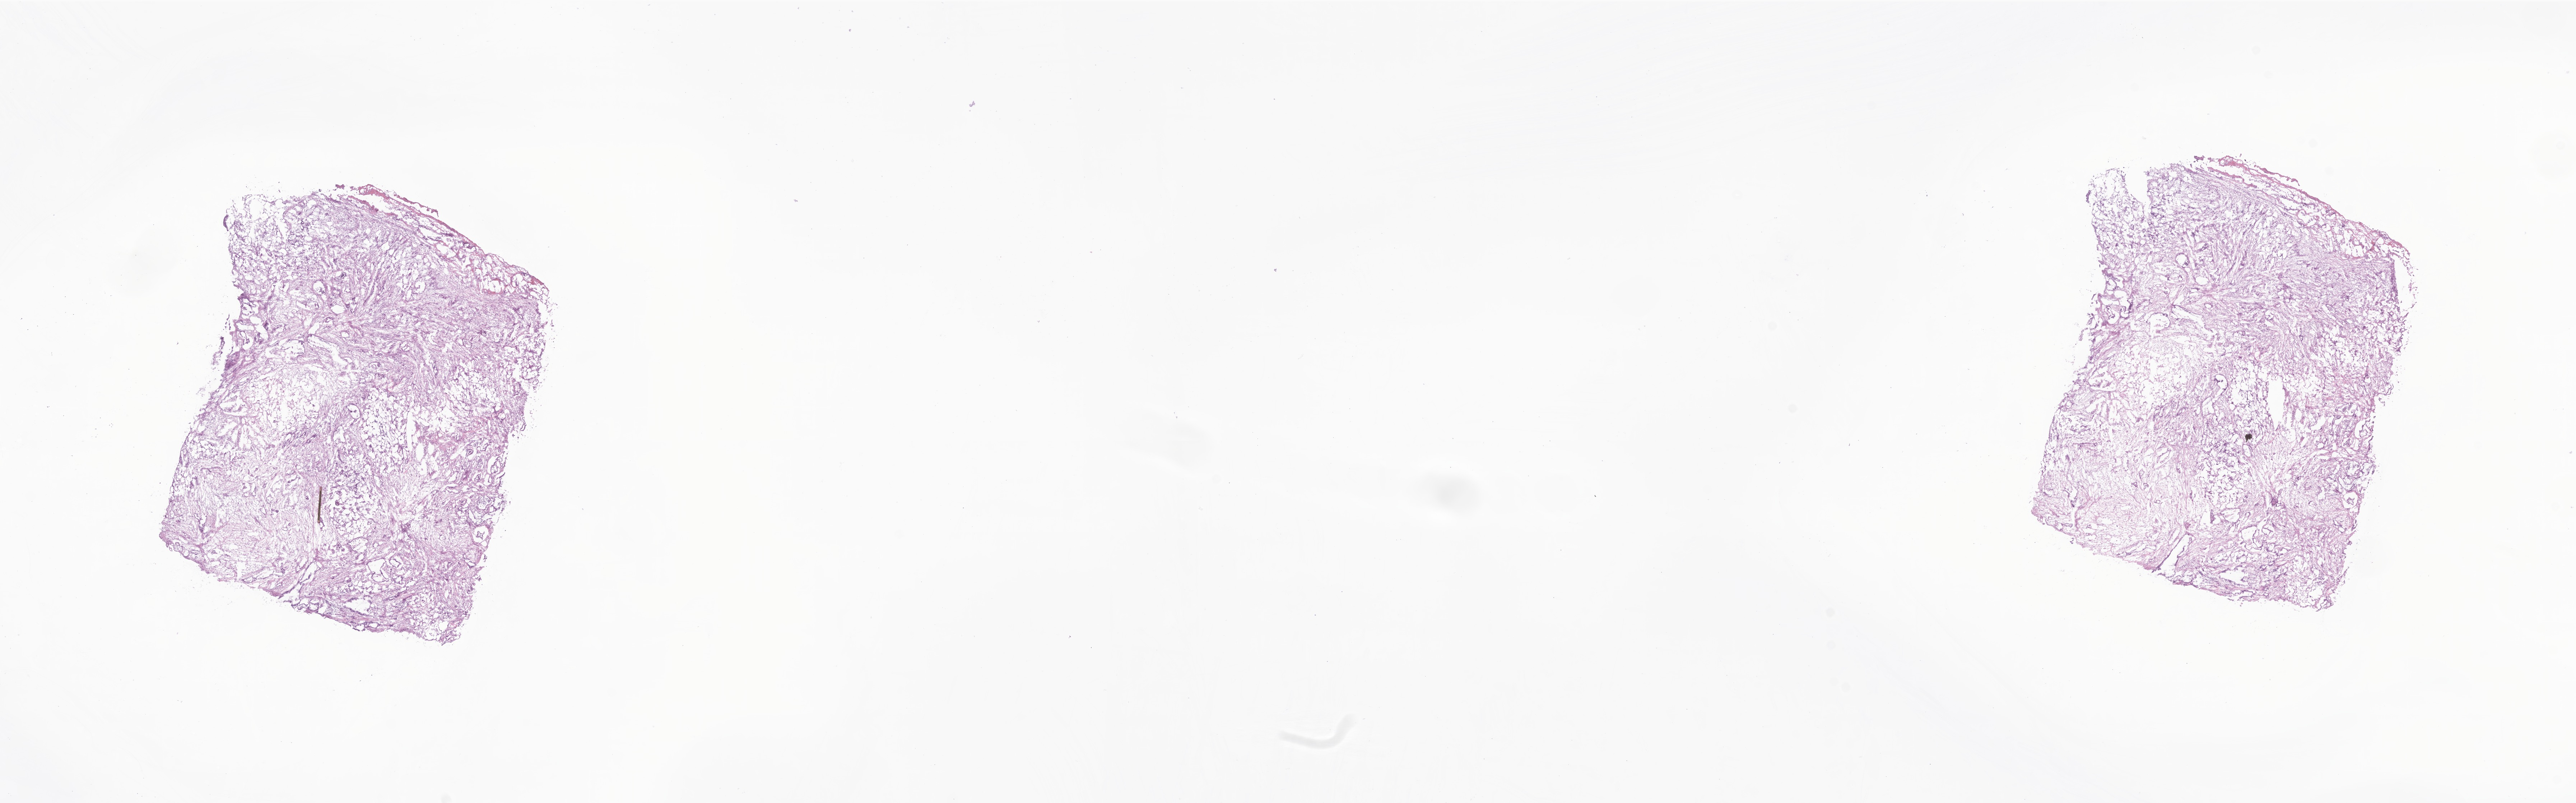
H&E whole-slide image of tumor tissue from the abdomen, low-resolution overview of the scanned area, about 30.2 x 9.4 mm; frozen section (OCT-embedded). Female patient, age 206 months (17 years 2 months).
* recorded diagnosis: Adenocarcinoma, metastatic, NOS